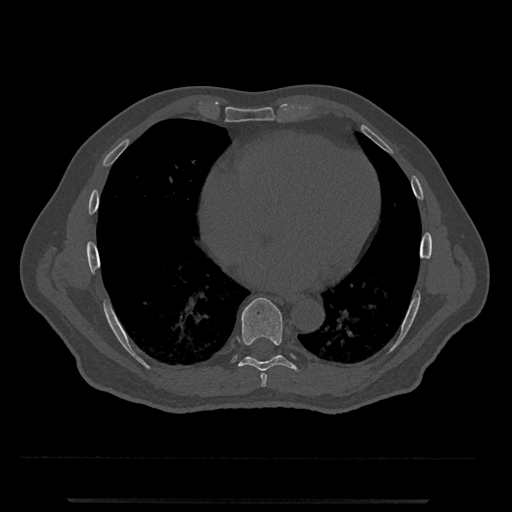
CT including the spine, one axial slice. Position 625 of 797 along the scan axis. Reconstruction kernel Br40s/3. 120 kVp. Bone window (W 1800 / L 400 HU). 0.5 mm slice thickness. 512 × 512 image matrix, field of view 419 × 419 mm. Male patient, age 63 years. From the clinical record (not read from this slice): primary cancer: prostate.
Annotated regions visible in this slice (semi-automatically segmented with operator editing):
- T7 vertebra: box from (x=260, y=373) to (x=267, y=387) px
- T8 vertebra: (x=231, y=298)–(x=298, y=371)